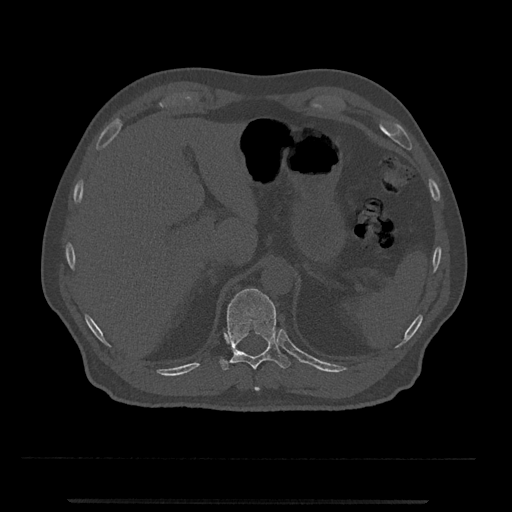
CT including the spine, one axial slice. Position 466 of 797 along the scan axis. 120 kVp. Bone window (W 1800 / L 400 HU). 0.5 mm slice thickness. 512 × 512 image matrix. Patient: male, 63 years. From the clinical record (not read from this slice): primary cancer: prostate.
Structures marked on this image (semi-automatic segmentation, software-assisted and operator-edited):
- T10 vertebra: box from (x=254, y=387) to (x=260, y=391) px
- T11 vertebra: (x=220, y=288)–(x=291, y=370)